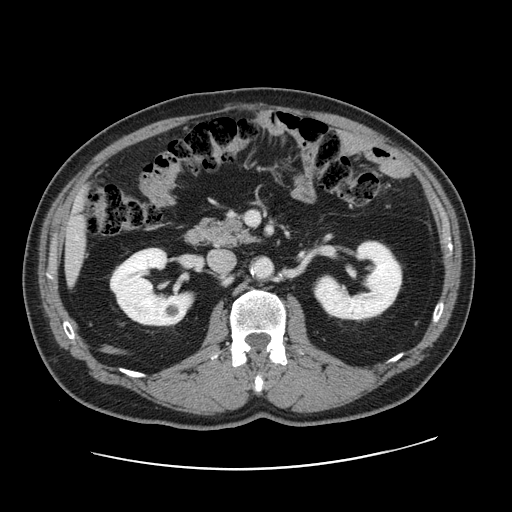
Contrast-enhanced abdominal CT, one axial slice. 120 kVp. Intravenous contrast given. Soft-tissue window (W 400 / L 40 HU). 2.5 mm slice thickness. 512 × 512 image matrix. Male patient, age 63 years. Case-level facts recorded for this patient, not image findings: diagnosis: colorectal cancer liver metastases, imaged before liver resection; multiple liver metastases: yes; largest metastasis: 8 cm.
Structures marked on this image (expert manual segmentation):
- liver: bounding box <67,212,86,276> (left, top, right, bottom; pixels)